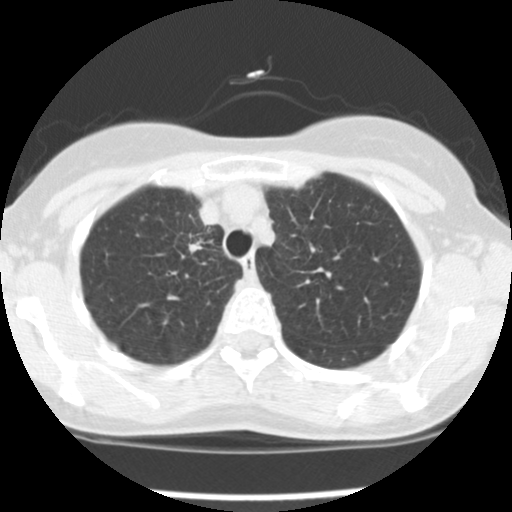
Low-dose screening chest CT, one axial slice; position 122 of 157 along the scan axis; 120 kVp; lung window (W 1500 / L -600 HU); 2.5 mm slice thickness; 512 × 512 image matrix.
Annotated regions visible in this slice (expert manual segmentation):
- lesion 1 (tumor, upper lobe of right lung): box from (x=188, y=241) to (x=203, y=254) px